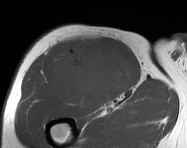
MRI of an extremity soft-tissue mass, one axial slice; slice 98 of 114 in the series (ordered by position); MR volume resampled by the dataset authors to the PET/CT grid (not the native acquisition matrix); 3.27 mm slice thickness; 187 × 148 image matrix. Male patient. From the clinical record (not read from this slice): histological type: pleiomorphic leiomyosarcoma; grade: intermediate; site of the primary tumour: right thigh.
Structures marked on this image (expert contour drawn on MRI and transferred to this co-registered scan by the dataset authors):
- gross tumour volume including surrounding oedema: bounding box [x1, y1, x2, y2] px = [50, 36, 133, 108]
- gross tumour volume (mass): [52, 38, 133, 108]